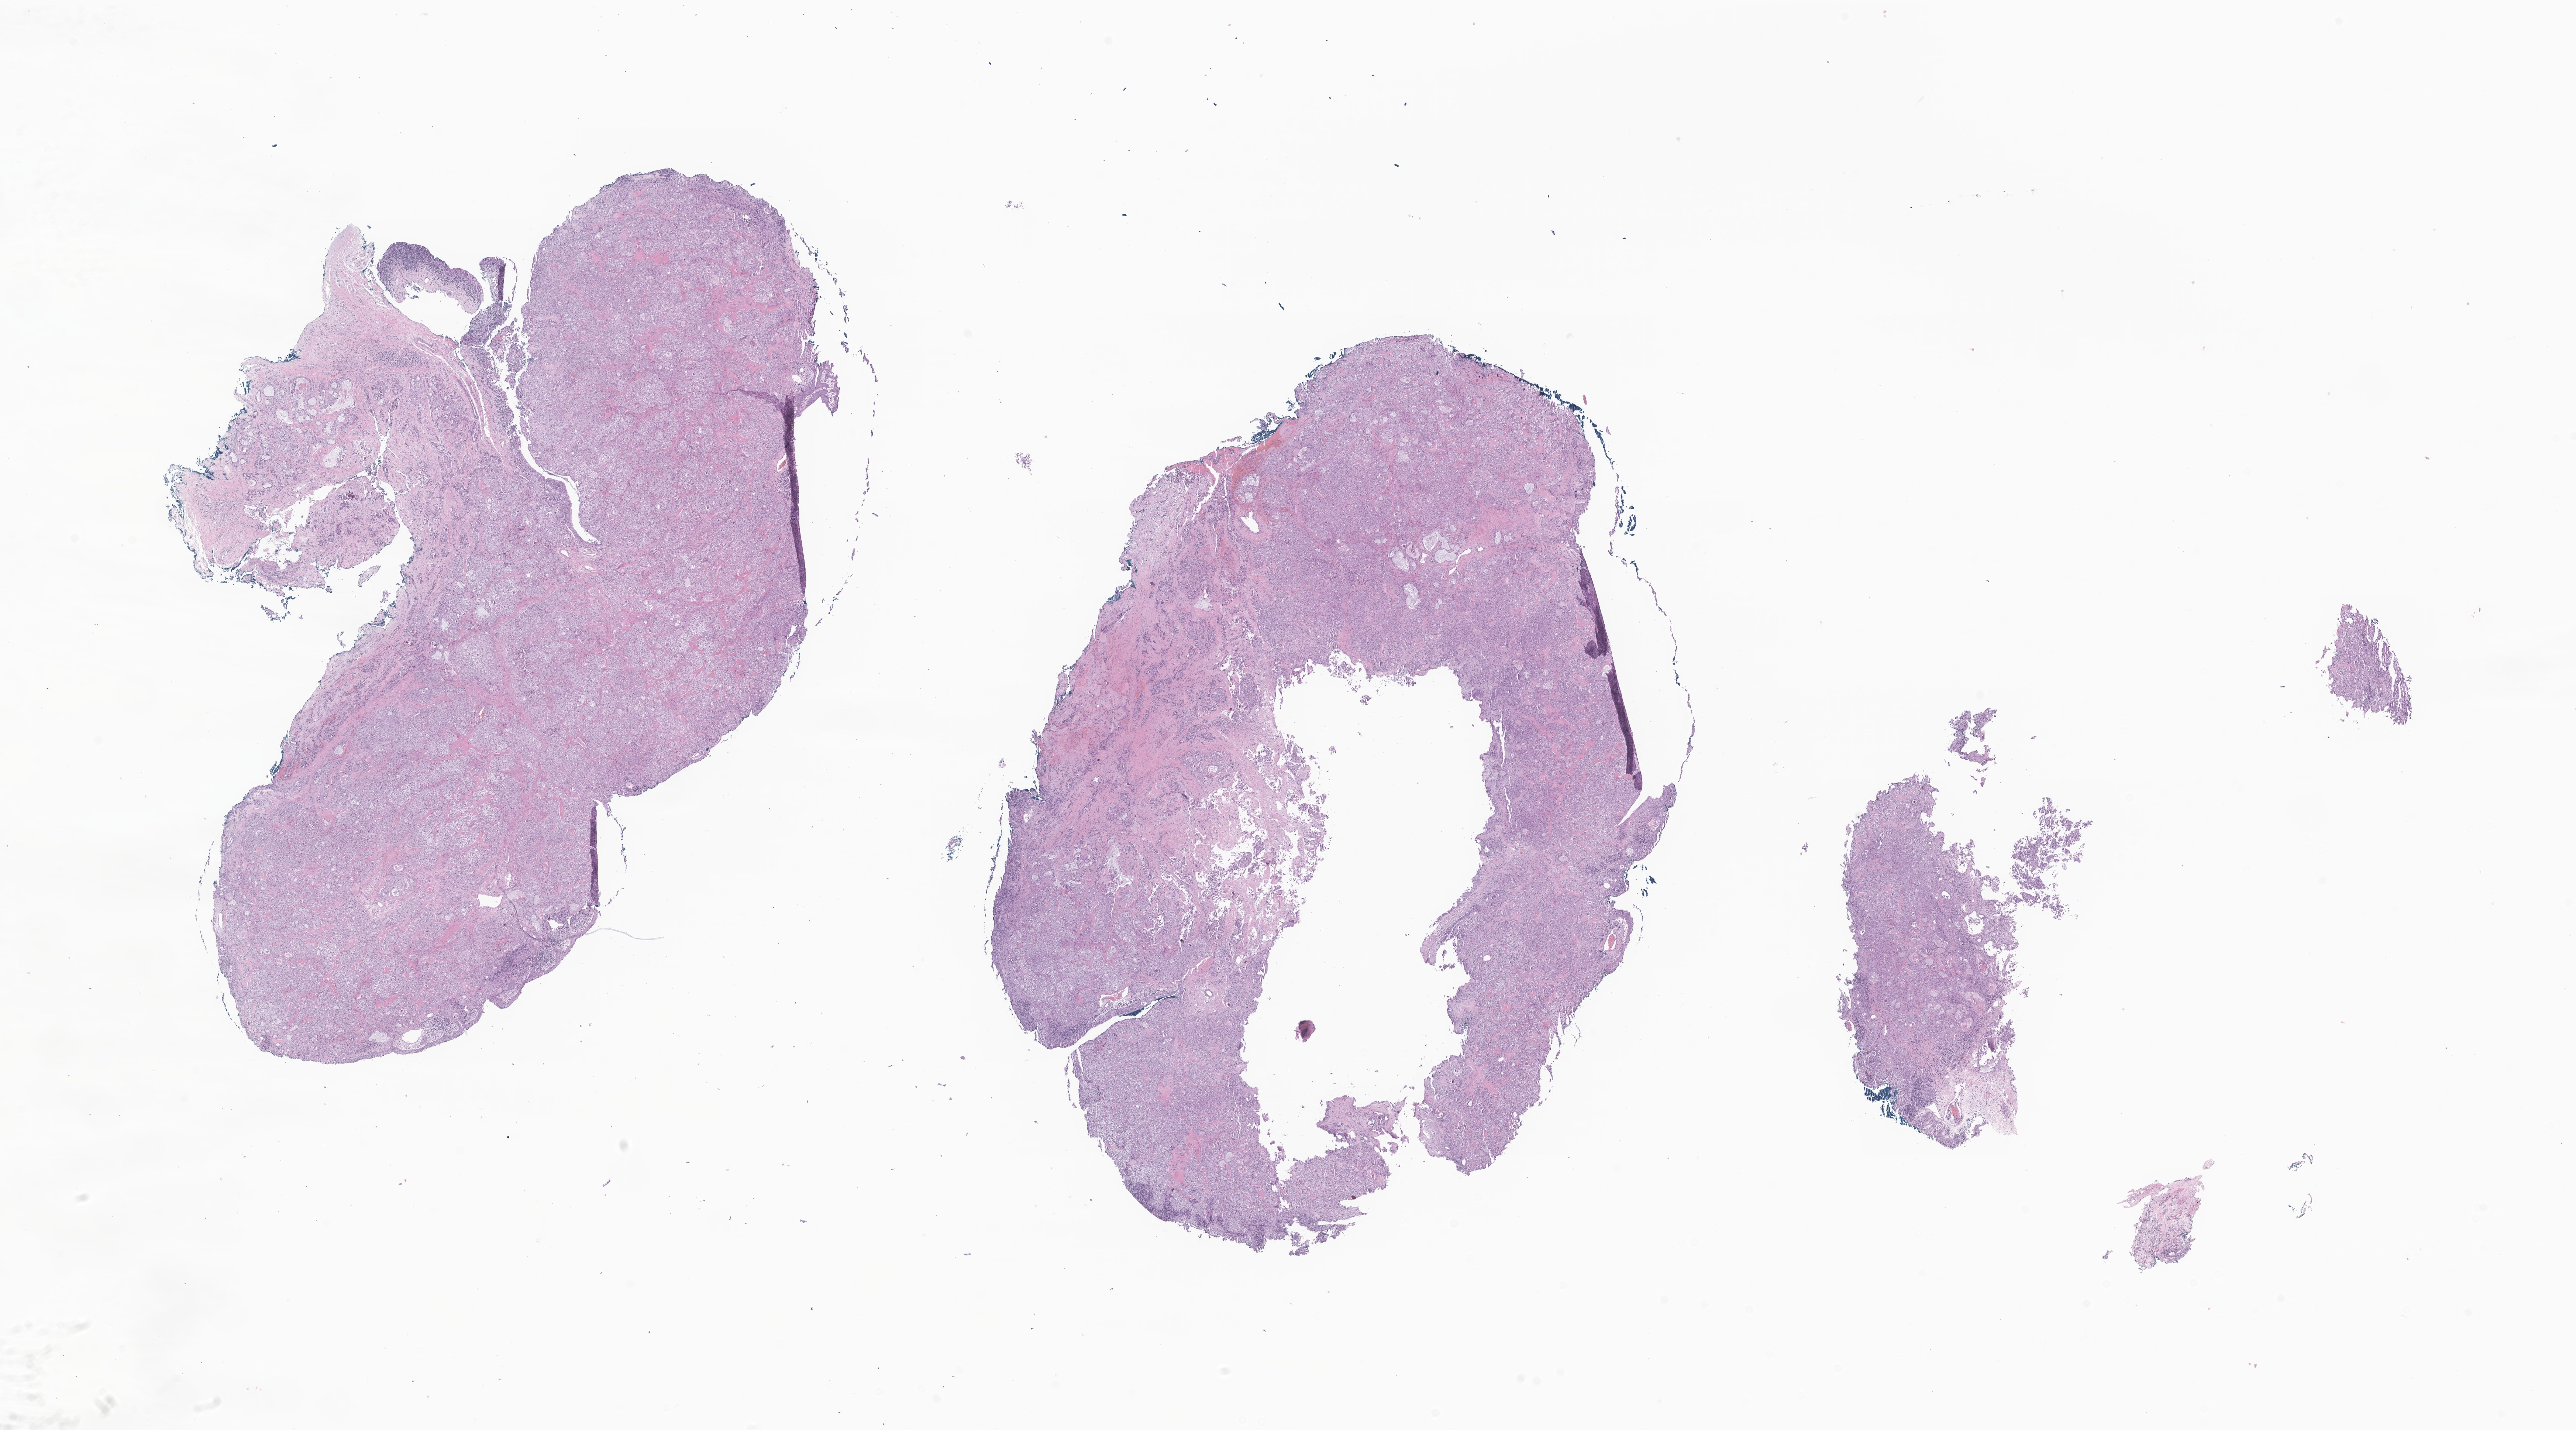
H&E whole-slide image of tumor tissue from the trachea — whole scanned area (about 29.4 x 16.3 mm) shown as a low-resolution overview. FFPE section. Patient male; age 86 months (7 years 2 months).
• recorded diagnosis: Mucoepidermoid carcinoma